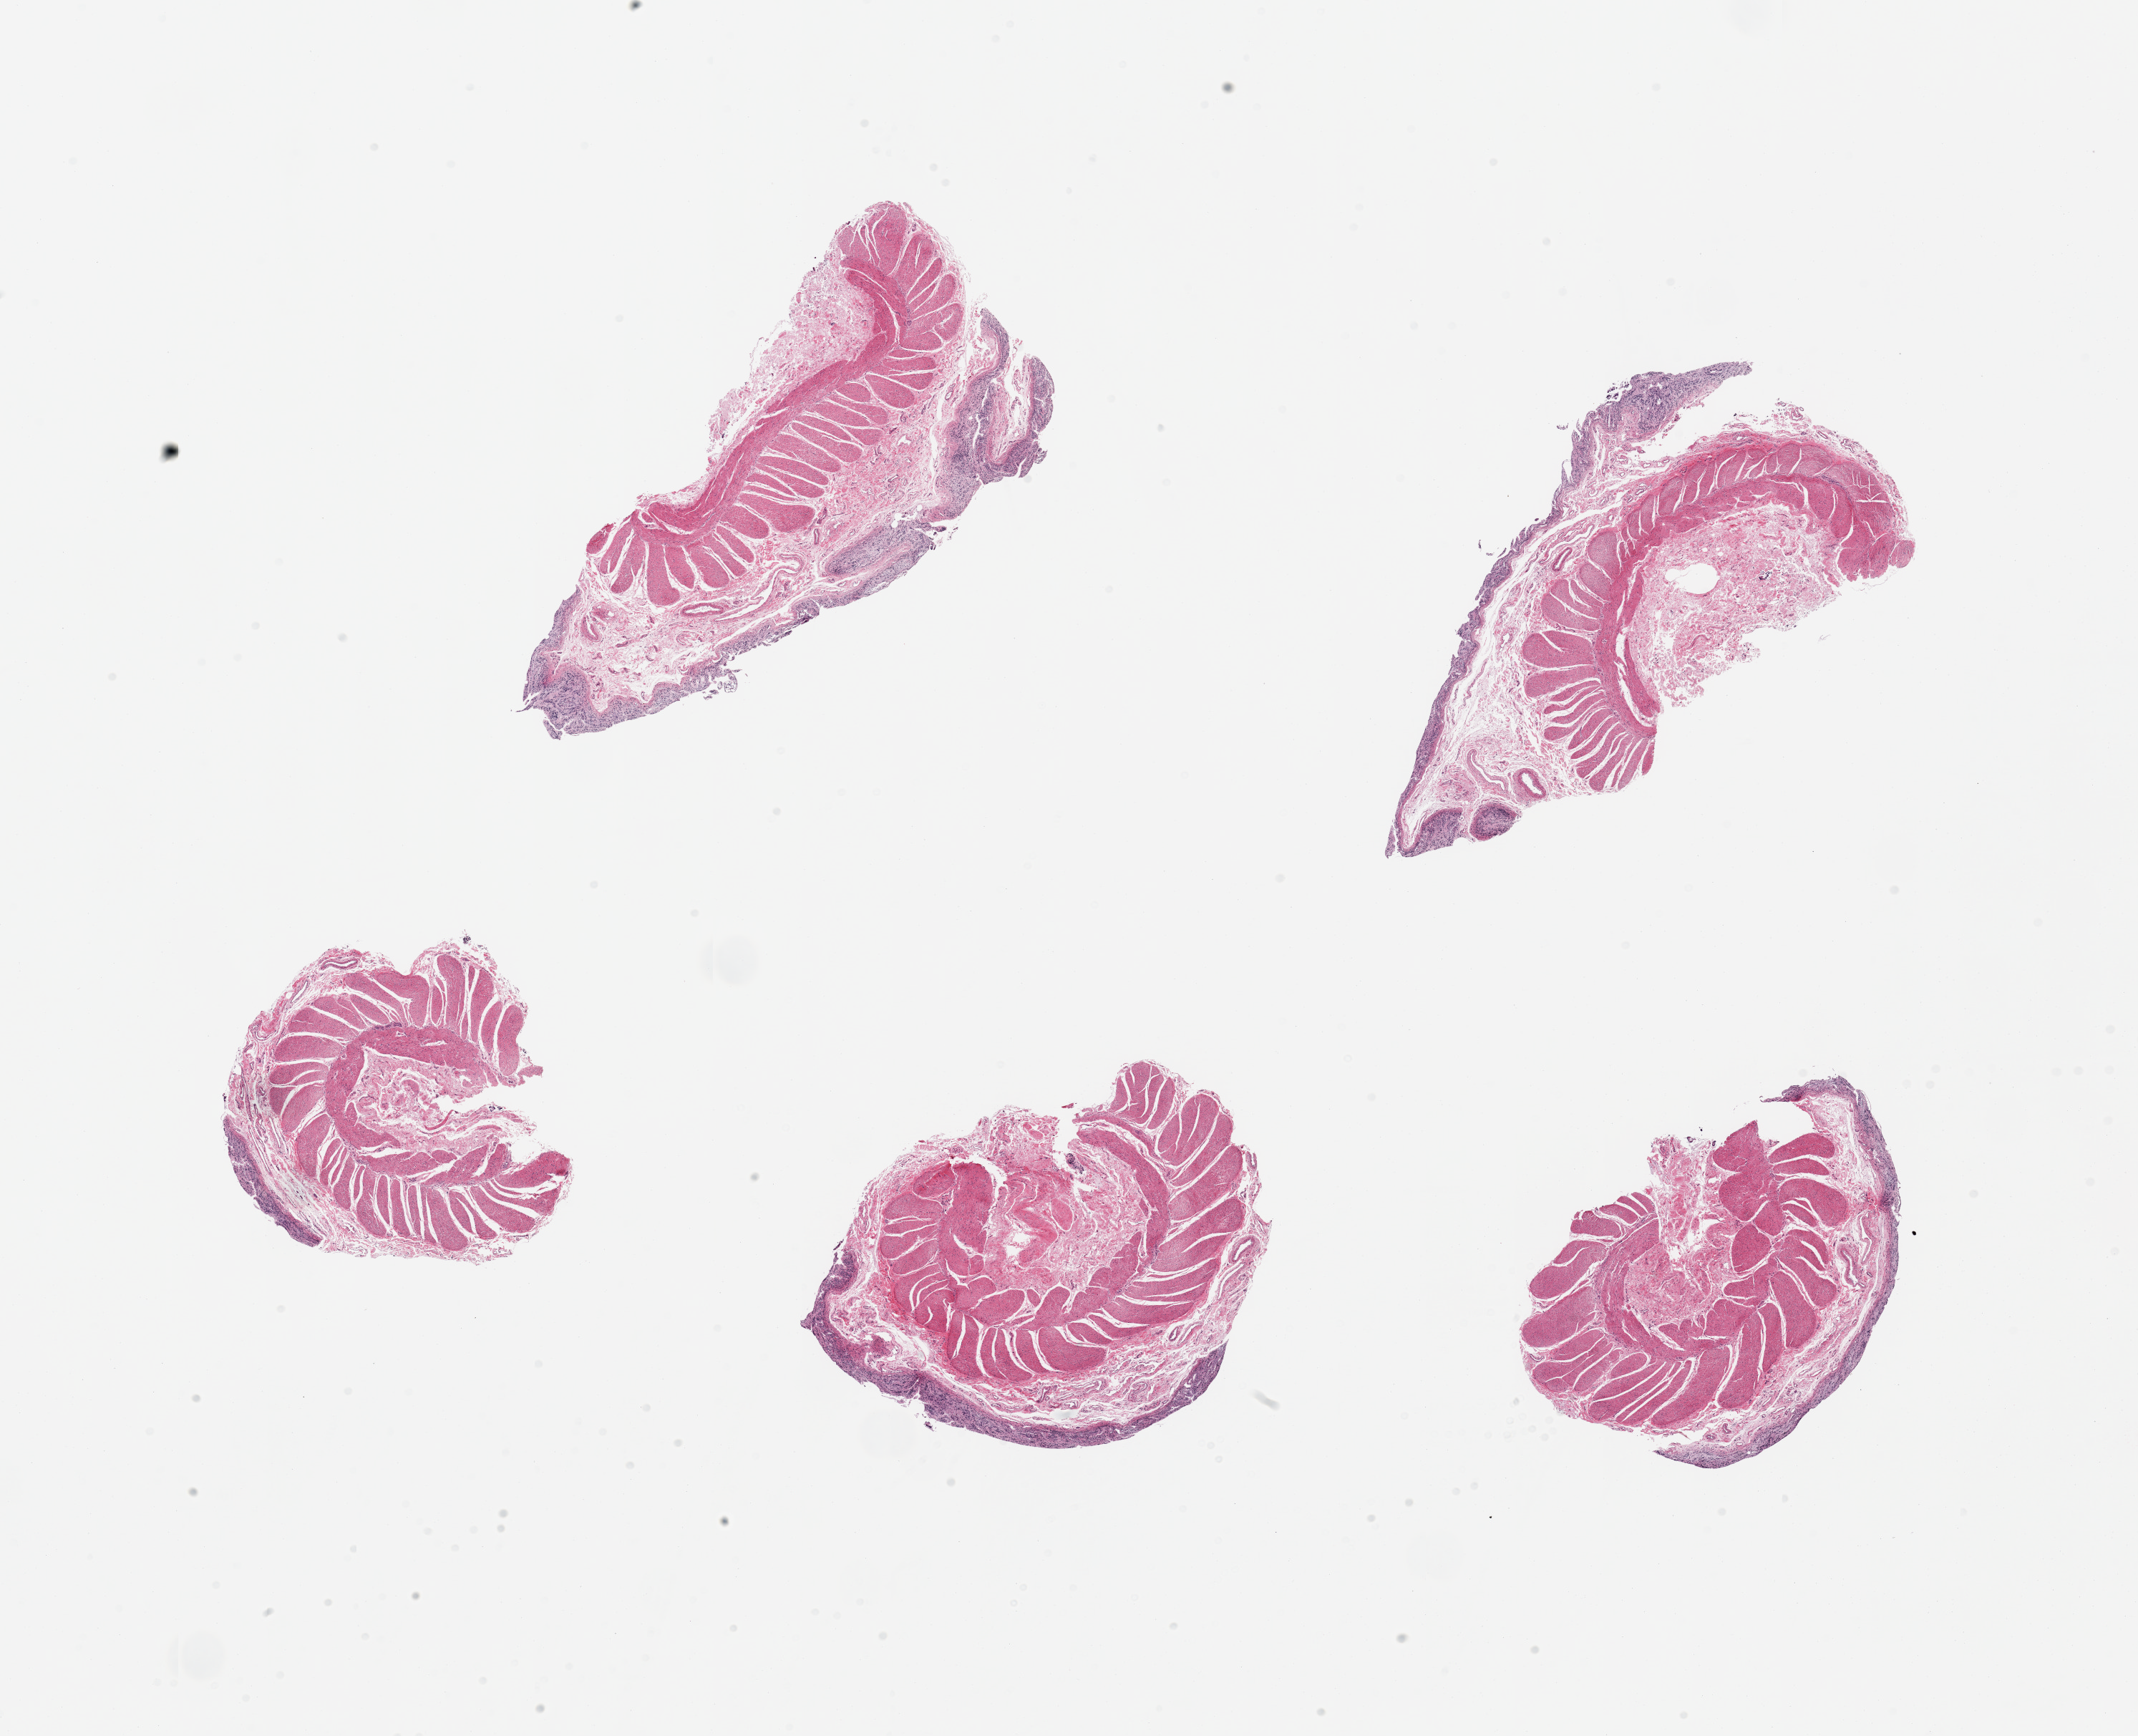
Digitized hematoxylin and eosin (H&E)-stained section, a low-resolution overview of the entire scanned area, about 23.6 x 19.2 mm. Donor sex: female.
* specimen: PAXgene-fixed, paraffin-embedded tissue; sampled site (target tissue): sigmoid colon; donor tissue sample